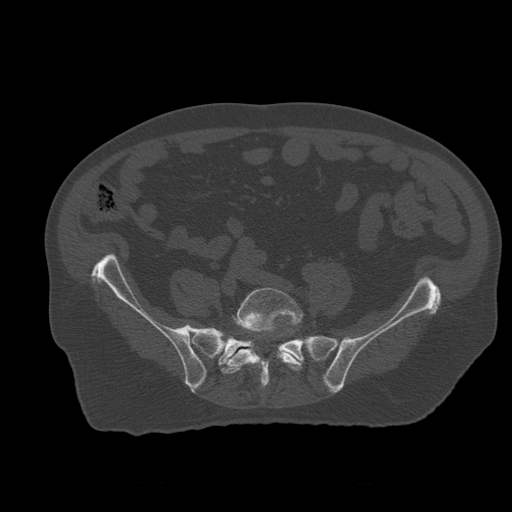
CT including the spine, one axial slice. Position 133 of 399 along the scan axis. Reconstruction kernel STANDARD. 120 kVp. Bone window (W 1800 / L 400 HU). 512 × 512 image matrix, field of view 407 × 407 mm. Patient age 73 years. From the clinical record (not read from this slice): primary cancer: prostate; vertebrae with lytic lesions (as recorded): L2.
Outlined on this slice (semi-automatically segmented with operator editing):
- L5 vertebra: bounding box (x1, y1, x2, y2) in pixels: (221, 288, 303, 388)